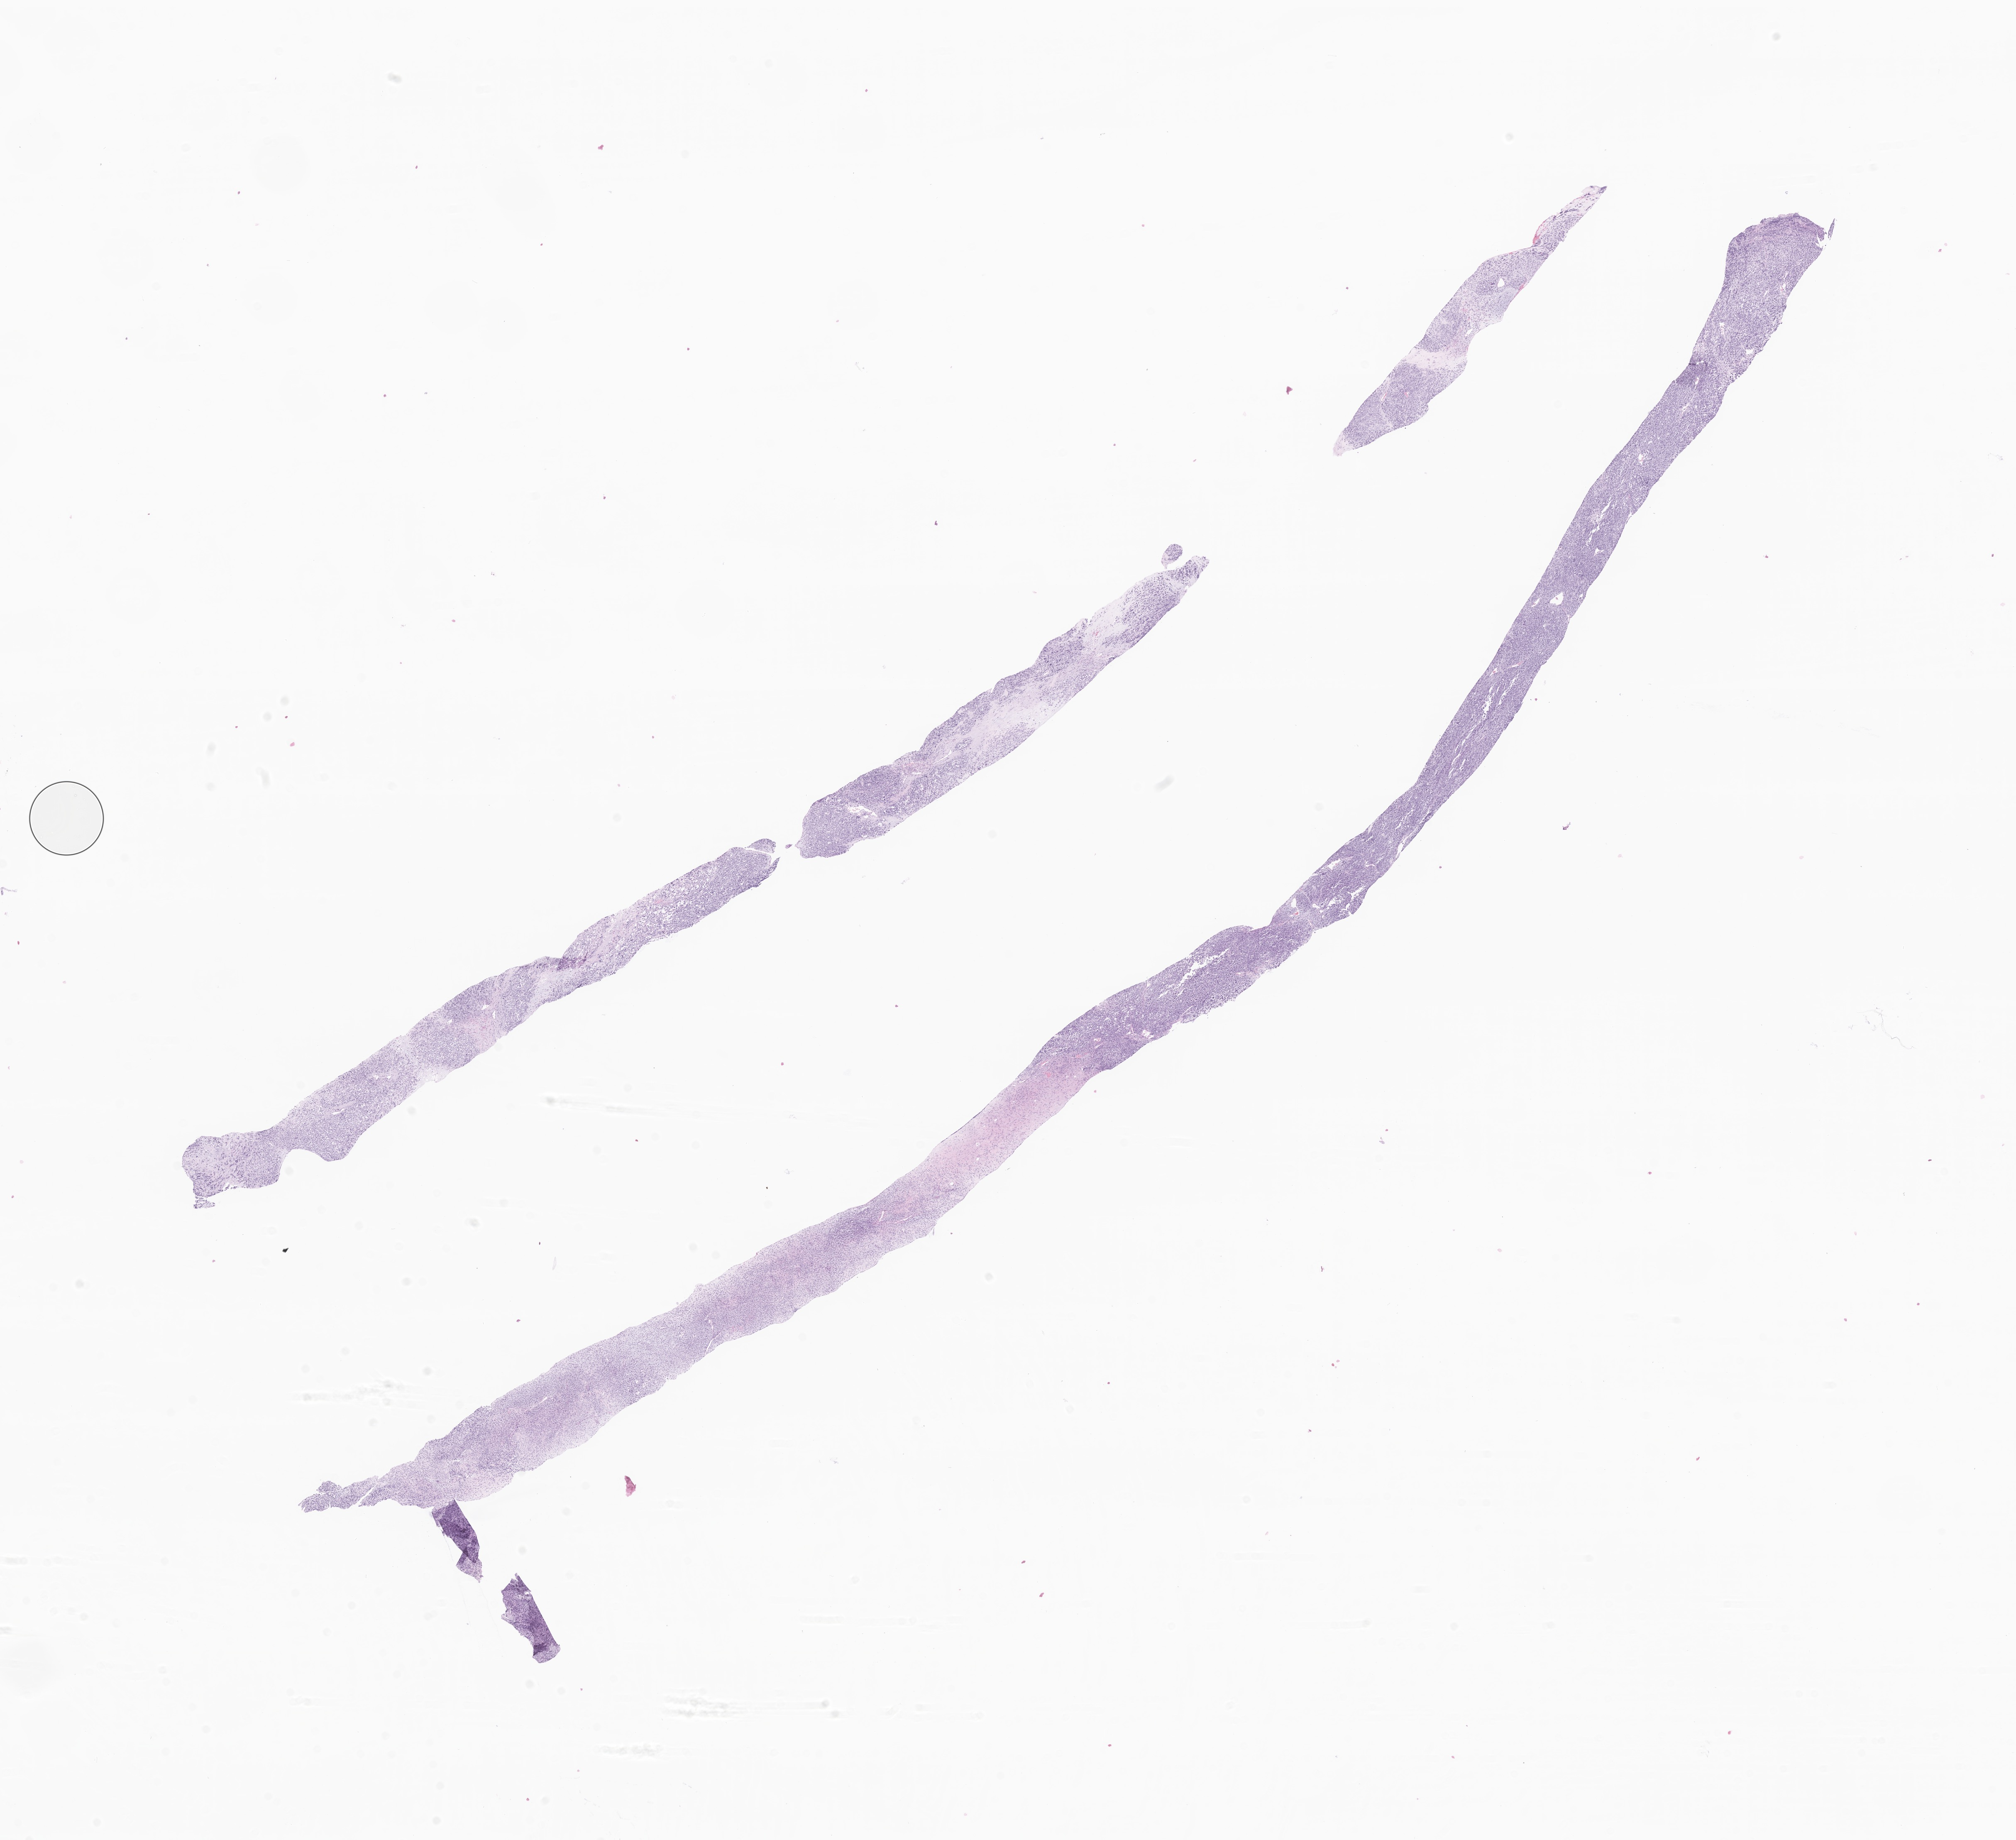
Whole-slide image, H&E stain of tumor tissue from the prostate, shown as a low-resolution overview of the whole scanned area (about 20.5 x 18.7 mm), formalin-fixed paraffin-embedded section. Patient: male, age 149 months (12 years 5 months).
Recorded diagnosis: Embryonal rhabdomyosarcoma, NOS.